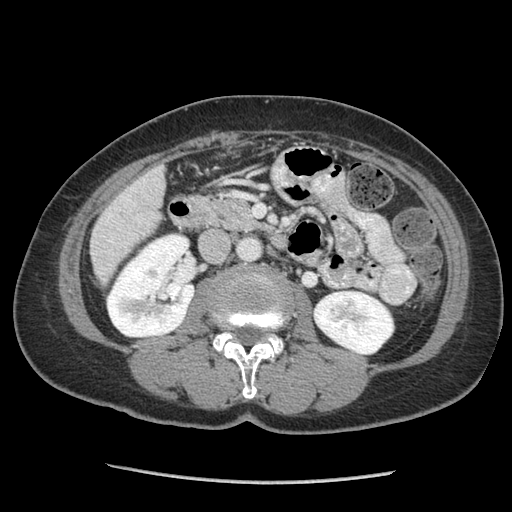
Contrast-enhanced abdominal CT (liver protocol), one axial slice; slice 23 of 105 in the series (ordered by position); reconstruction kernel STANDARD; soft-tissue window (W 400 / L 40 HU); 2.5 mm slice thickness; 512 × 512 image matrix, field of view 340 × 340 mm. From the clinical record (not read from this slice): diagnosis: hepatocellular carcinoma (patient treated with transarterial chemoembolisation; whether this scan precedes or follows treatment is not stated here); TNM stage (as recorded): Stage-I; Child-Pugh class: A; tumour differentiation: moderately differentiated; tumour nodularity: uninodular.
Annotated regions visible in this slice (semi-automatic segmentation, software-assisted and operator-edited):
- liver parenchyma outside the tumour (the mass and vessels are separate outlines, so this box may not span the whole liver): box from (x=90, y=164) to (x=164, y=282) px
- liver vessels: (x=108, y=199)–(x=131, y=242)